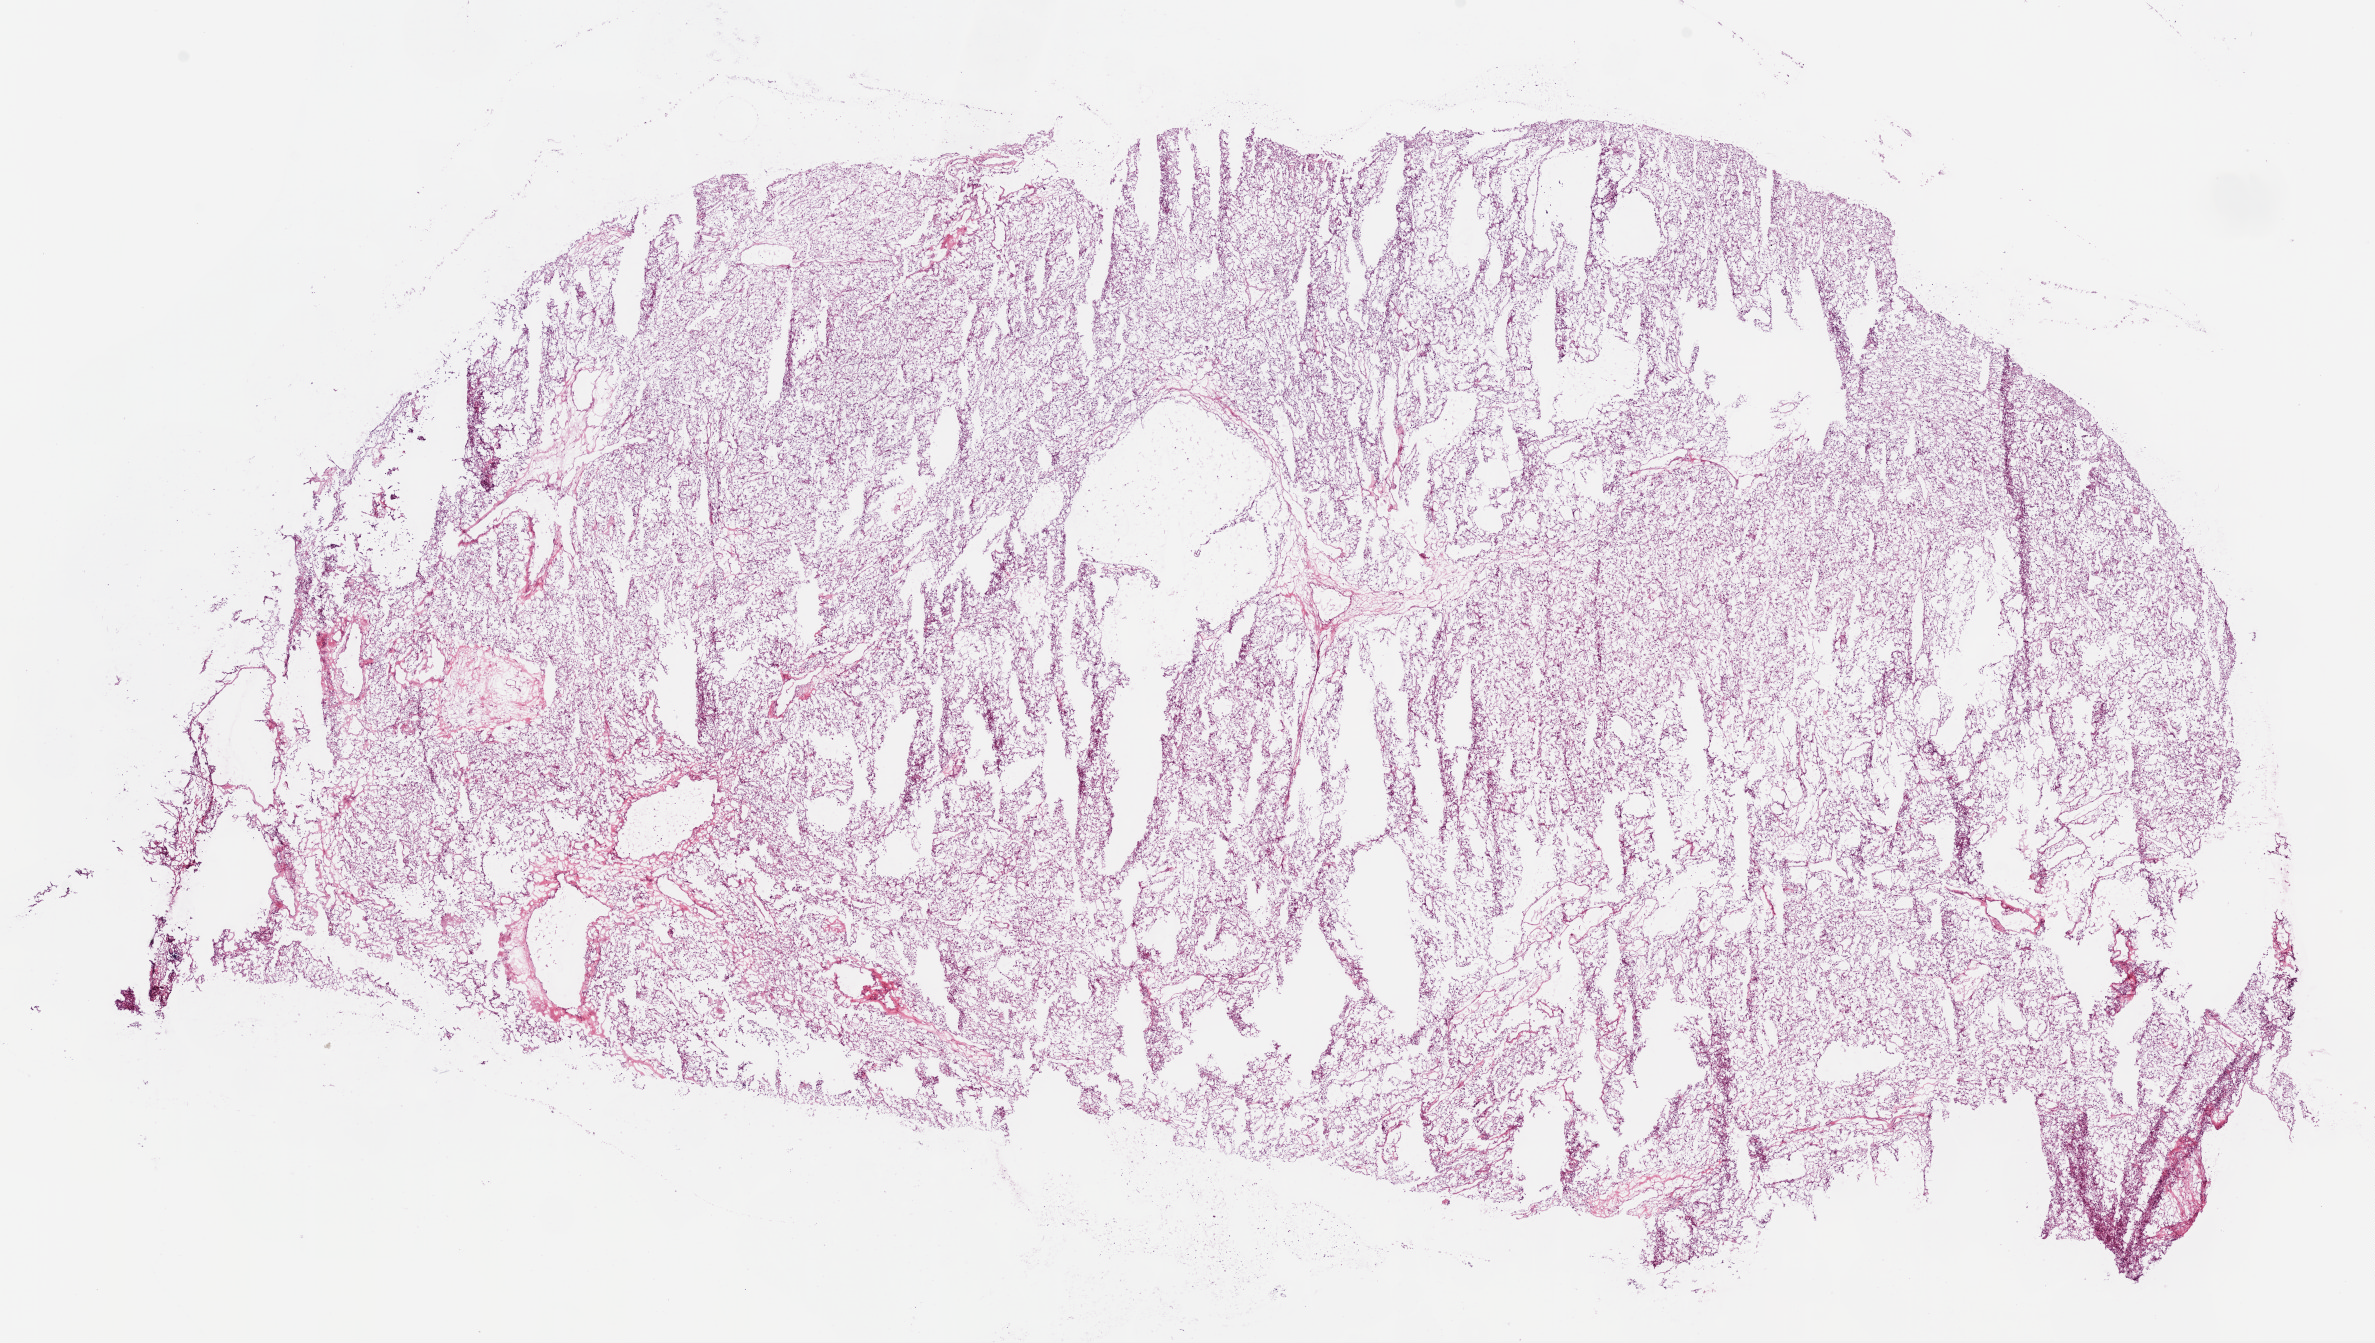
Whole-slide histology image, H&E-stained, whole scanned area (about 19.1 x 10.8 mm, slide scanned at 20x) shown as a low-resolution overview. Frozen section from the bottom of the tissue portion. Kidney, primary tumour sample. Male, age 52 years at initial diagnosis. Histologic grade: G3 (poorly differentiated). Composition of this section per pathologist review: tumour cells 90%, tumour nuclei 85%, normal cells 0%, stromal cells 10%, necrosis 0%.
TNM: T3b N0 M0. AJCC pathologic stage: III. Diagnosis: Clear cell adenocarcinoma, NOS. Laterality: right.